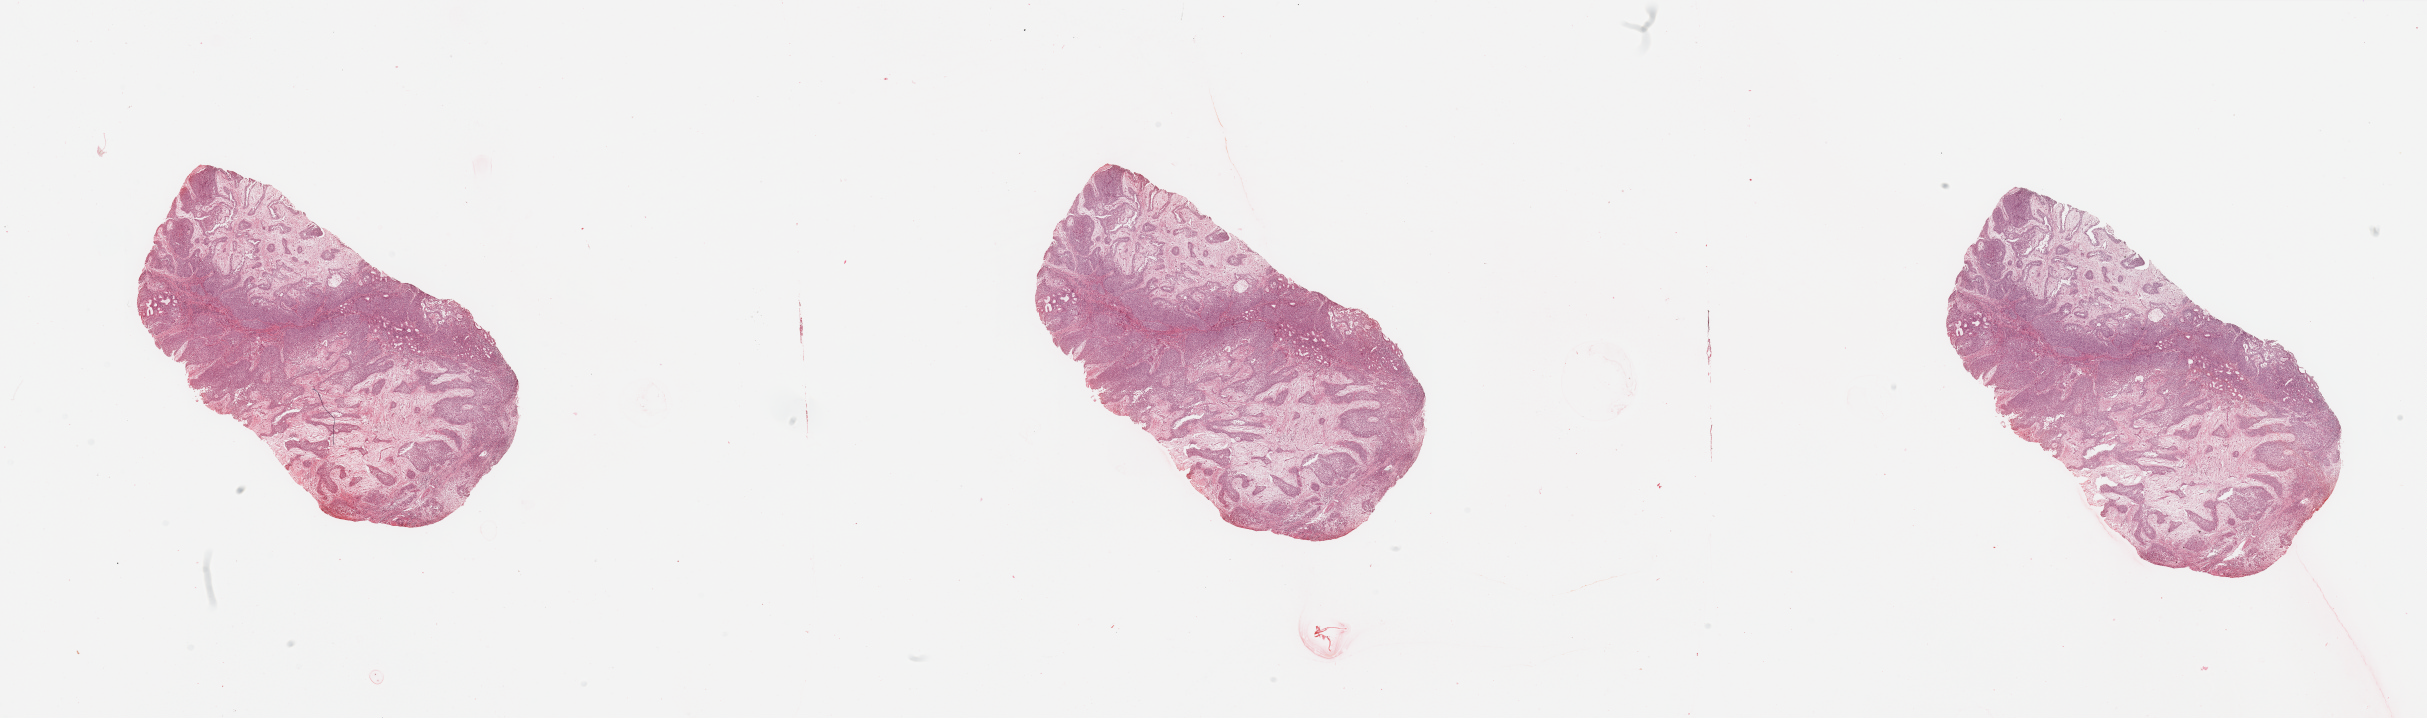
Digitized Hematoxylin and eosin (H&E) stained tissue section (whole slide) — shown as a low-resolution overview of the whole scanned area (about 38.4 x 11.4 mm, slide scanned at 20x). Tumour tissue sample, sampled site: larynx. 60-year-old male patient. Histologic grade: G3 (poorly differentiated). Pathologist review of this section (percent, as recorded): tumour nuclei 80%, necrosis 0%.
Primary tumour site (as recorded): larynx. Diagnosis: Squamous cell carcinoma, NOS (larynx, NOS). AJCC pathologic stage: II.